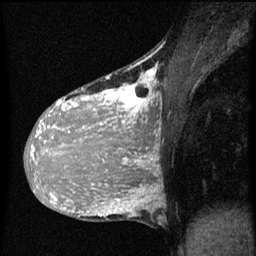
Breast MRI (dynamic contrast-enhanced), one sagittal slice; slice 27 of 60 in the series (ordered by position); dynamic contrast-enhanced series, image 2 of 3 at this slice position (ordered by acquisition); 1.5 T; TE 4.2 ms, TR 8 ms; 2 mm slice thickness; 256 × 256 image matrix. Patient: female, 36 years.
Annotated regions visible in this slice (semi-automatic segmentation, software-assisted and operator-edited):
- analysis volume of interest (the breast-tissue region the enhancement analysis was run in; not a lesion): bounding box <32,68,163,161> (left, top, right, bottom; pixels)
- tumour enhancement mask (voxels above the 70 % enhancement threshold inside the analysis volume of interest): <32,68,159,161>